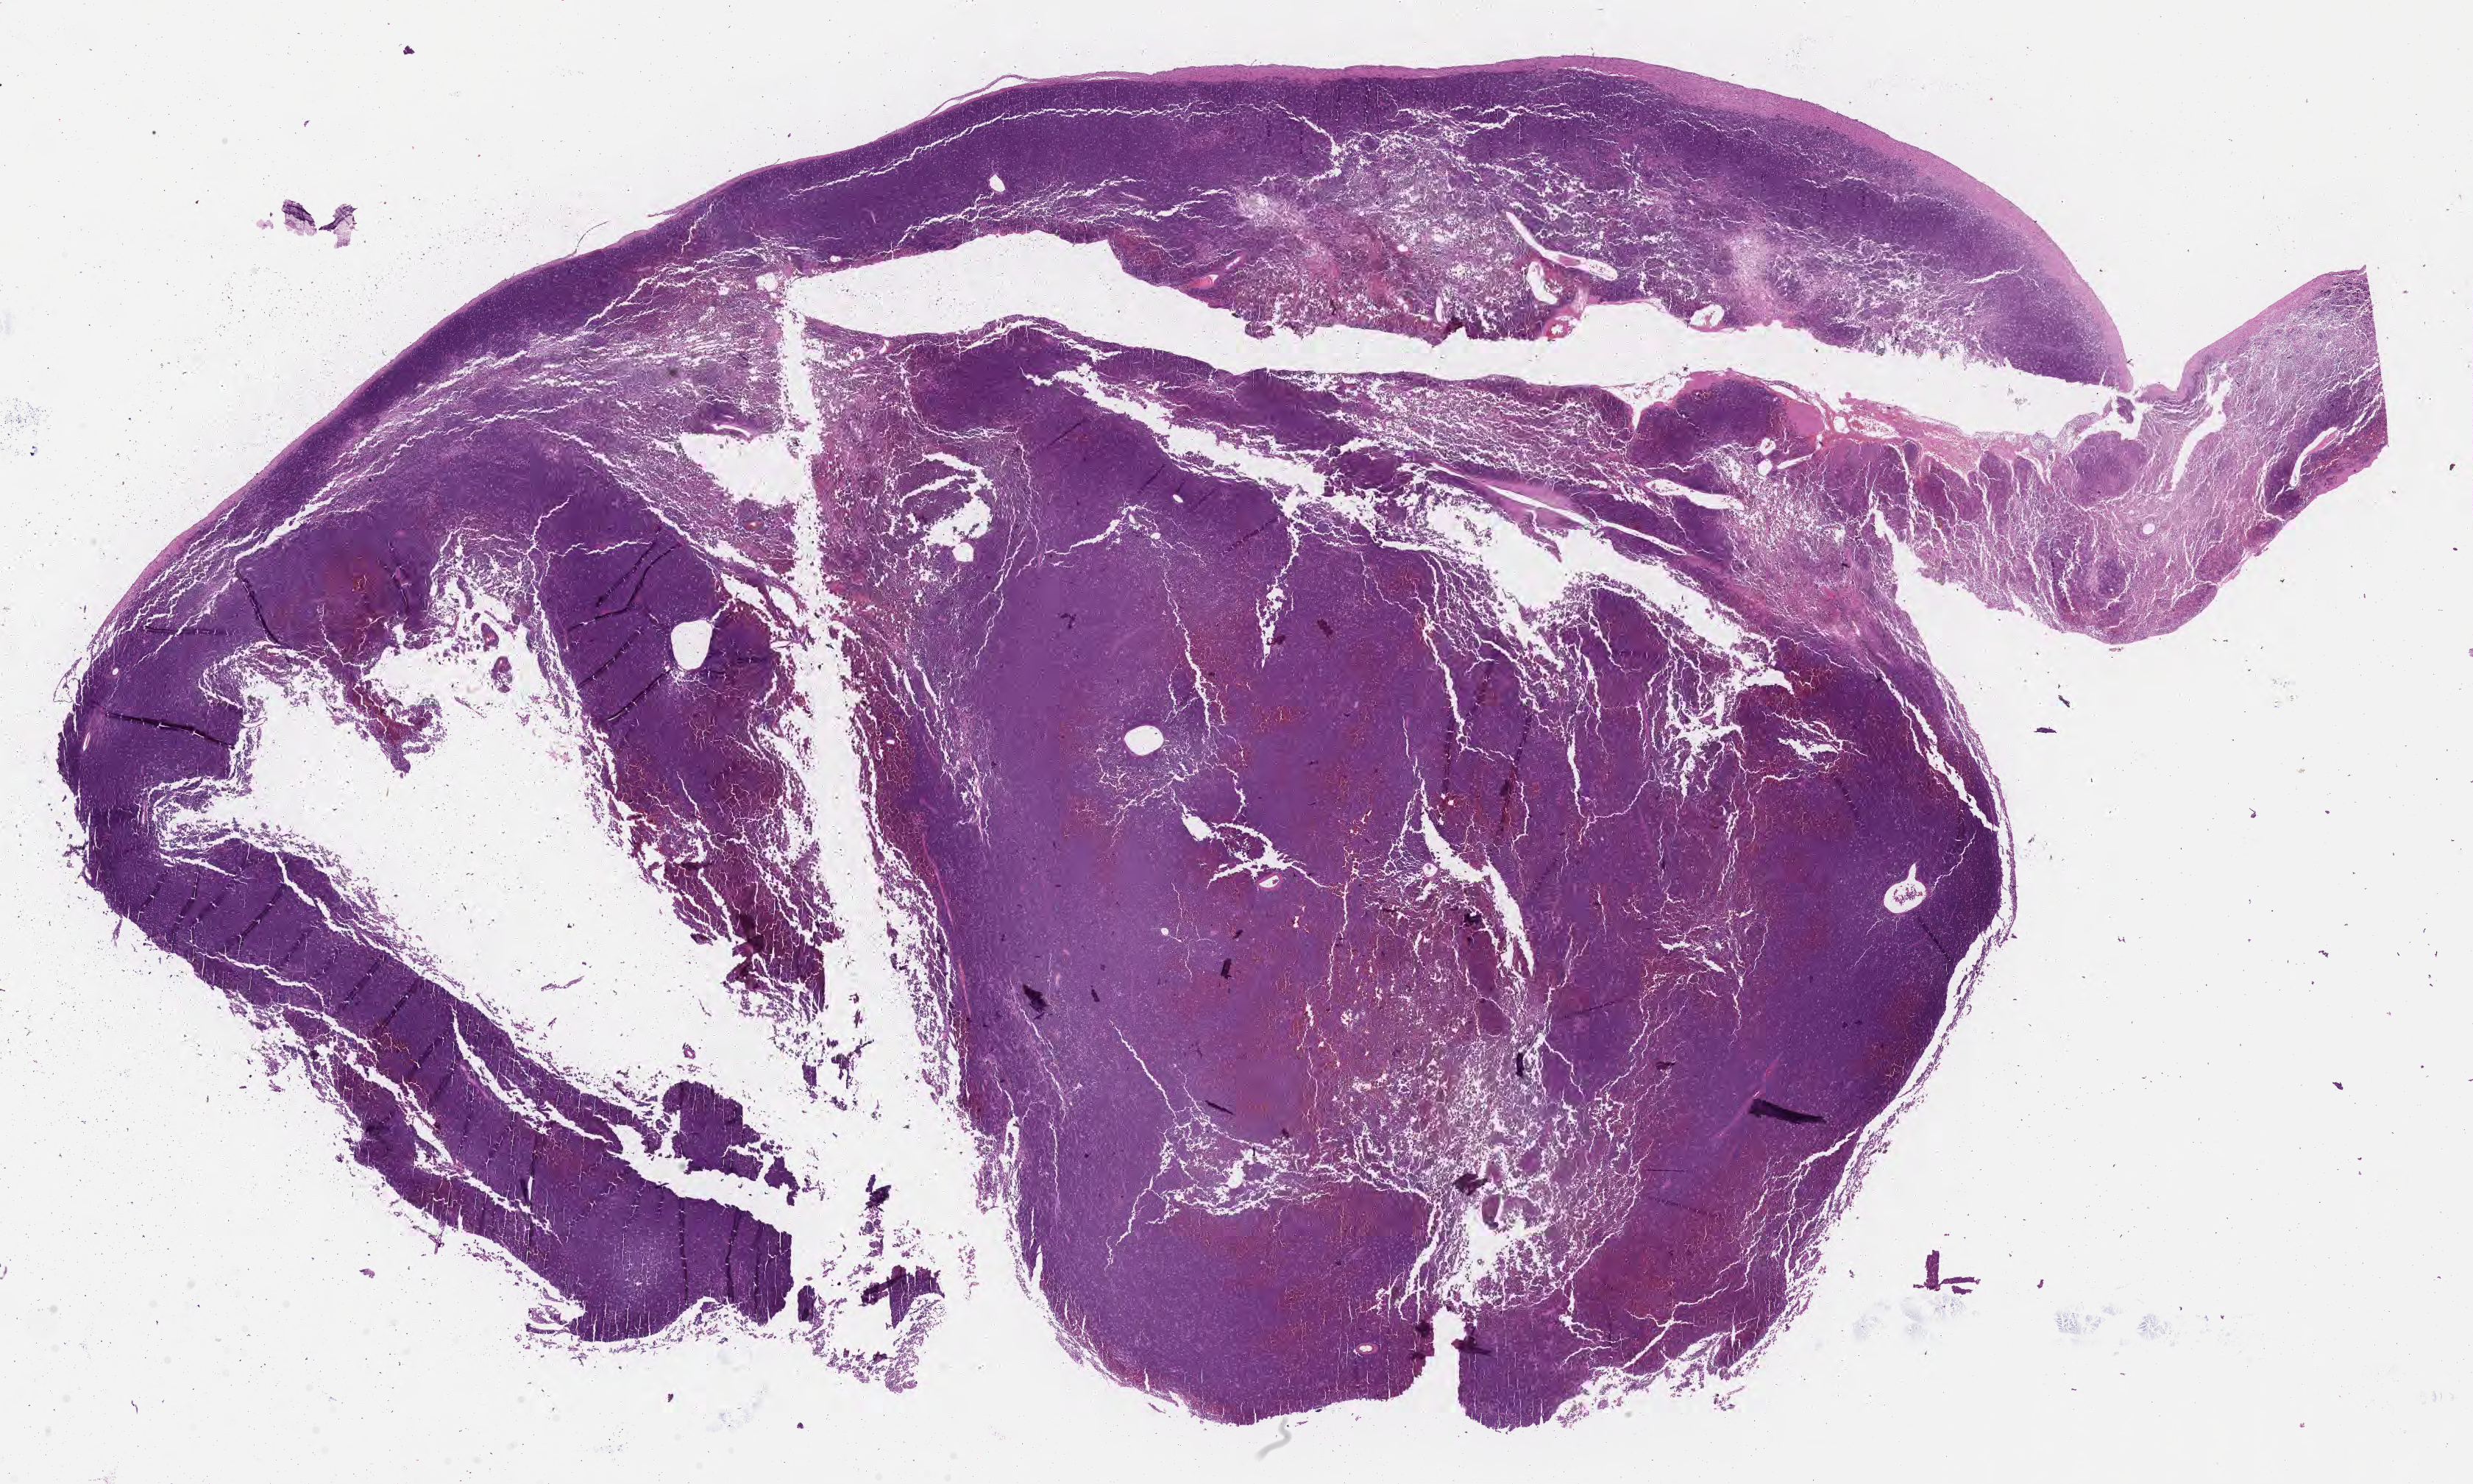
Digitized H&E-stained section, a low-resolution overview of the entire scanned area, about 27.2 x 16.3 mm. Formalin-fixed, paraffin-embedded (FFPE) tissue. Specimen: primary tumor. Female, age 3 years at initial diagnosis. Pathologist review of this section (percent, as recorded): tumor cells 85%, tumor nuclei 90%, stromal cells 5%, necrosis 0%, normal cells 10%. Inflammatory infiltration, as recorded: lymphocyte infiltration 70%, monocyte infiltration 20%, neutrophil infiltration 0%.
Histologic diagnosis: Burkitt lymphoma, NOS. Section: top of the tissue portion. Ann Arbor stage (patient): Stage IV.